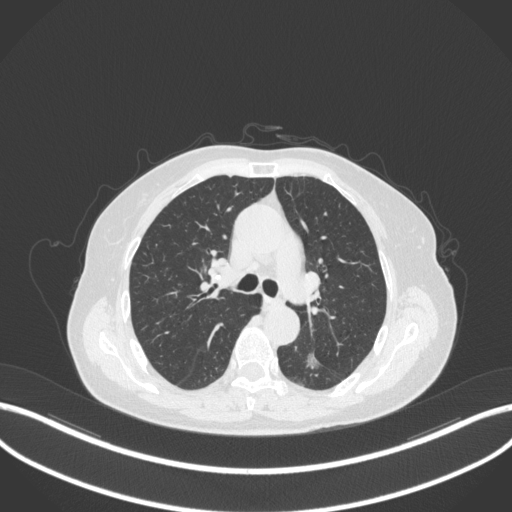
Chest CT, one axial slice. Slice 197 of 352 in the series (ordered by position). 120 kVp. Lung window (W 1500 / L -600 HU). 512 × 512 image matrix, field of view 400 × 400 mm. Patient: female, 70 years. Case-level facts recorded for this patient, not image findings: clinical TNM (as recorded): T1c N0 M0.
Annotated regions visible in this slice (rectangle marked by the reading radiologist):
- lung tumour (recorded histology: adenocarcinoma): bounding box [x1, y1, x2, y2] px = [301, 344, 323, 372]